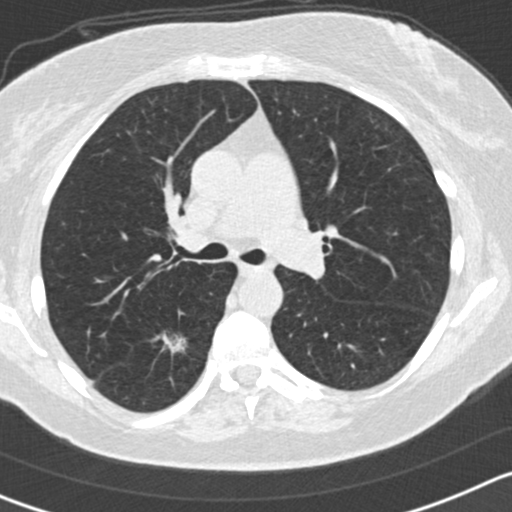
Low-dose screening chest CT, axial slice, baseline screening round, lung window (W 1500 / L -600 HU), 2 mm slice thickness, 120 kVp, slice 61 of 161 in the series. Female, age 65 years at enrolment. Former smoker at enrolment.
Lesion marked by an expert reader, bounding box [x1, y1, x2, y2] px = [137, 316, 198, 375]. Reader record for this screening exam (exam-level; its link to the box is not recorded): non-calcified nodule or mass ≥4 mm, right lower lobe, 14 × 13 mm, spiculated (stellate) margins, mixed attenuation. Official screen result: positive, change unspecified: nodule(s) >= 4 mm or enlarging nodule(s), mass(es), or other non-specific abnormalities suspicious for lung cancer. Later outcome: lung cancer diagnosed 565 days after this screen — adenocarcinoma, NOS, right lower lobe, moderately differentiated (G2), stage IA (AJCC 6th edition), 25 mm at pathology.